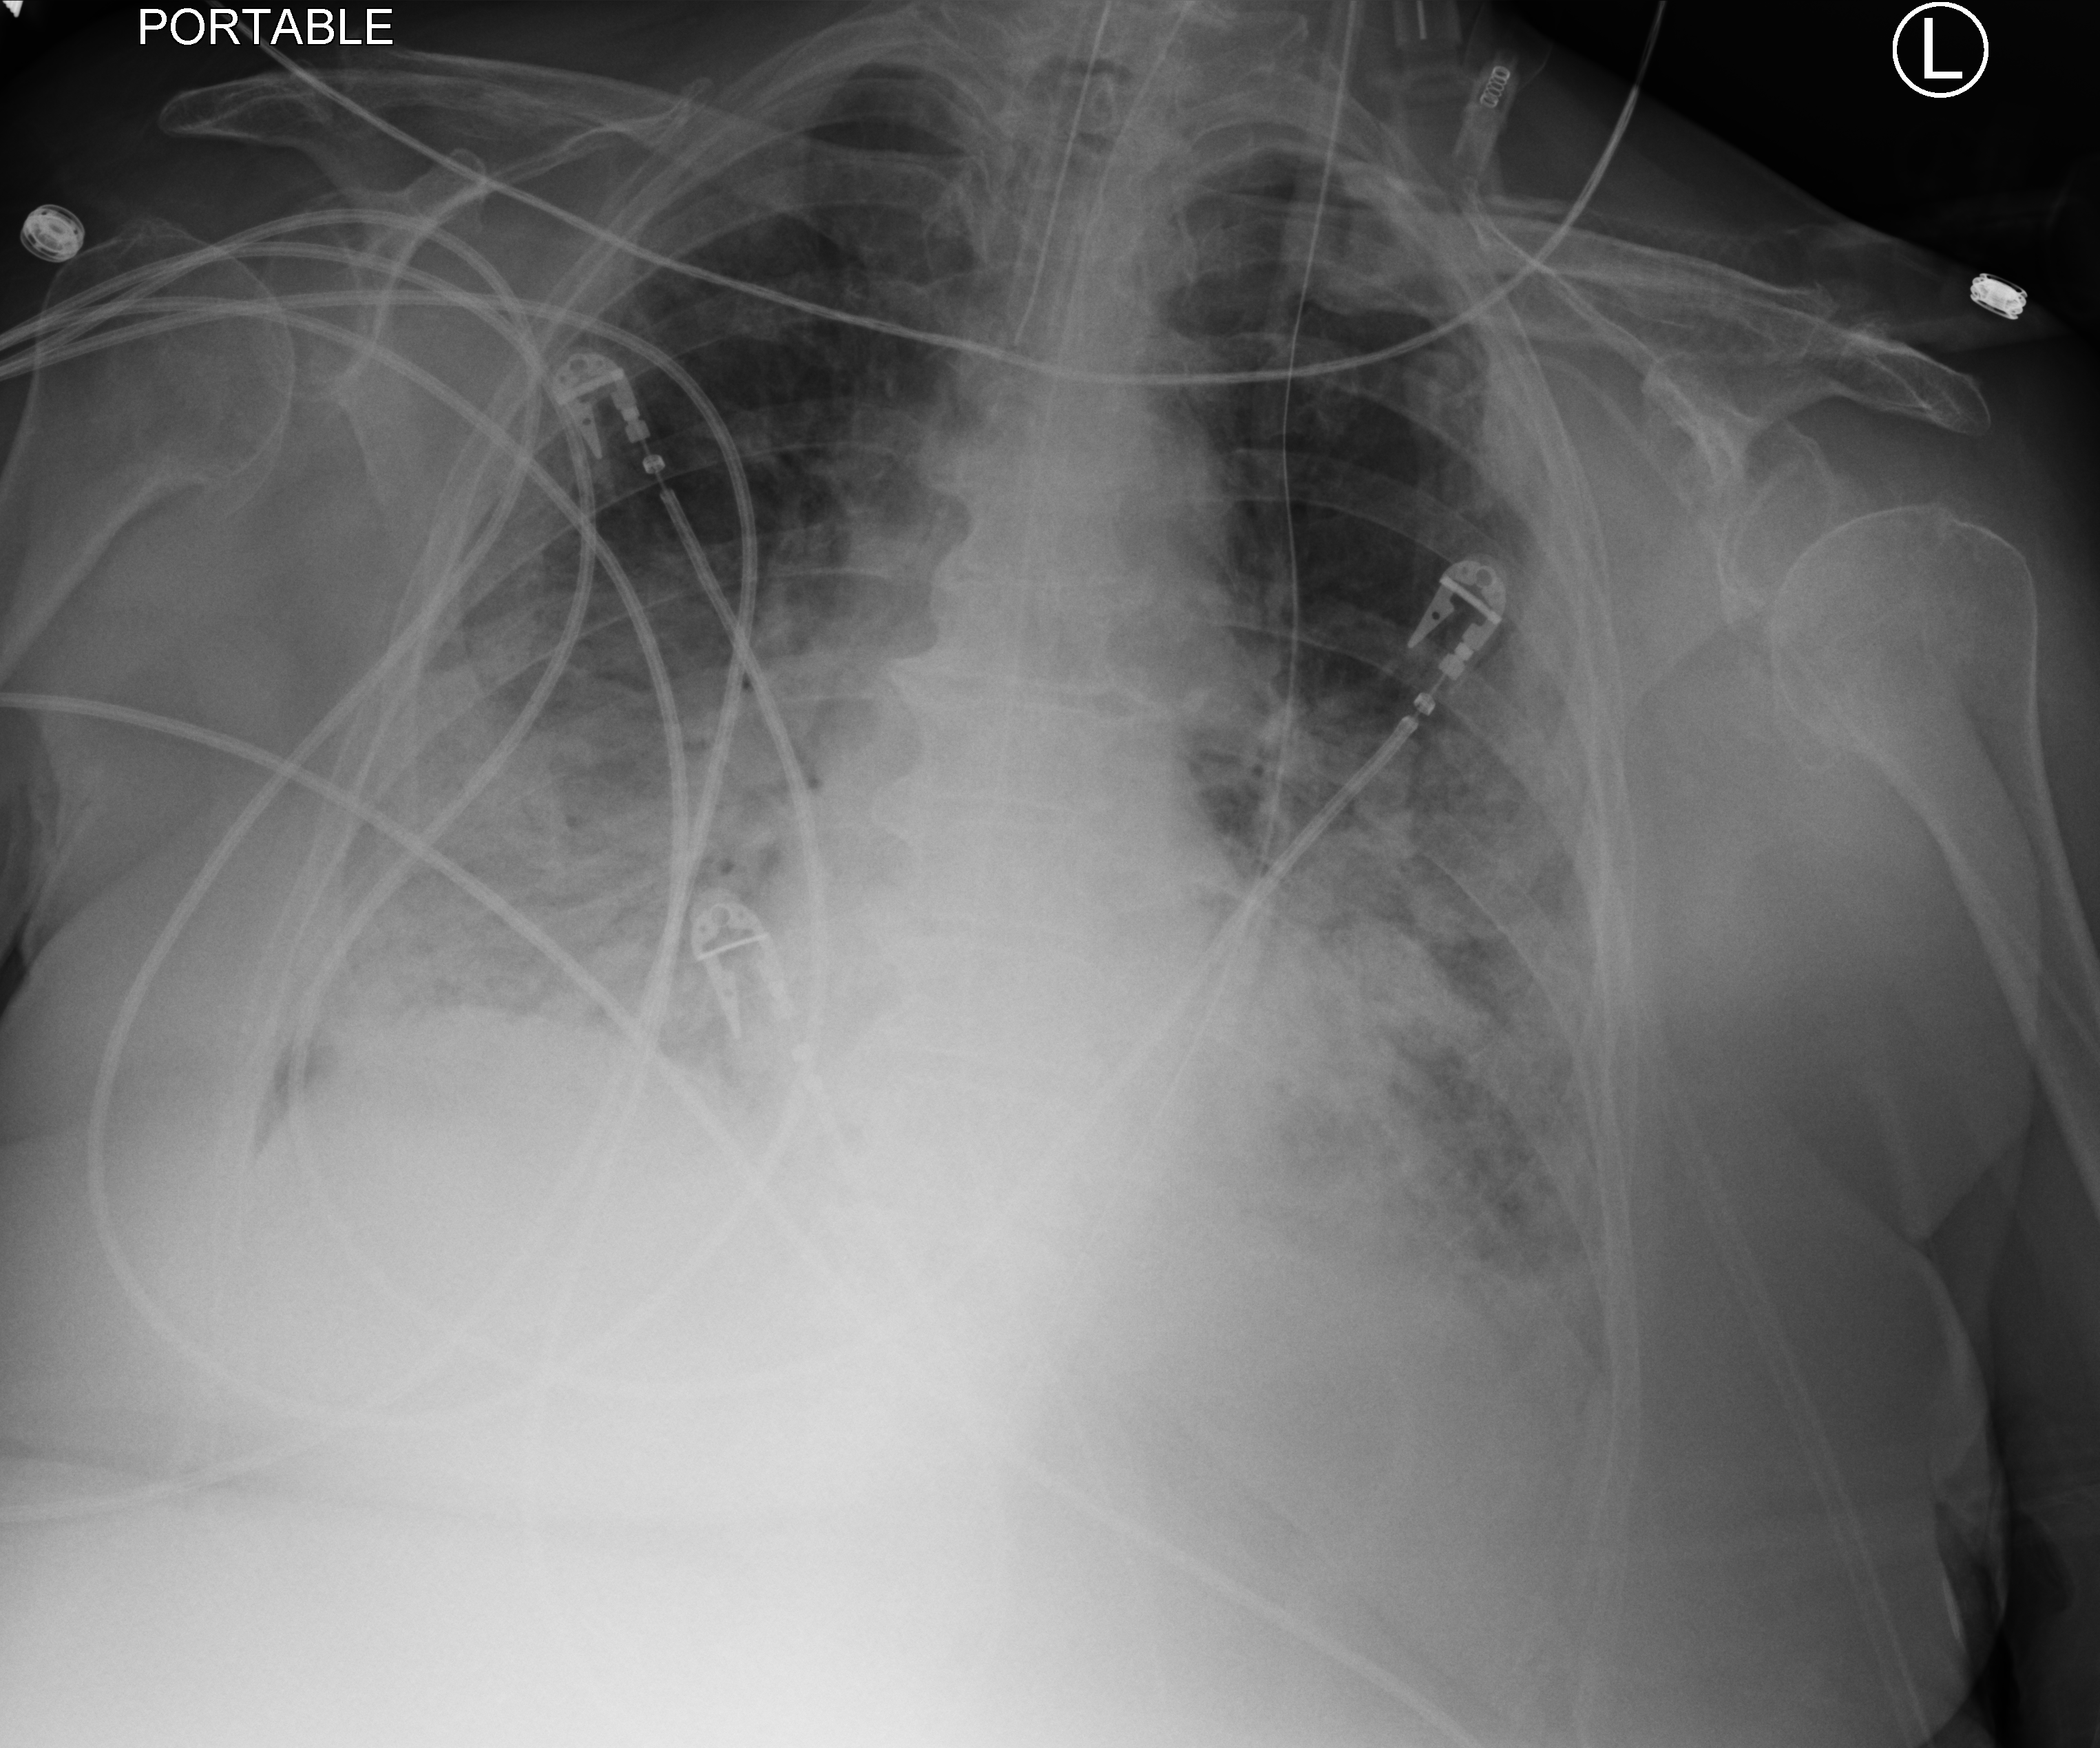
Portable chest radiograph. Female patient hospitalised with COVID-19, age 75–90 years.
From the hospital-stay record, not from the radiograph (when in the stay this image was taken is not recorded): mechanically ventilated during this hospital stay: yes; chronic kidney disease (admission record): no; admitted to intensive care during this hospital stay: no.